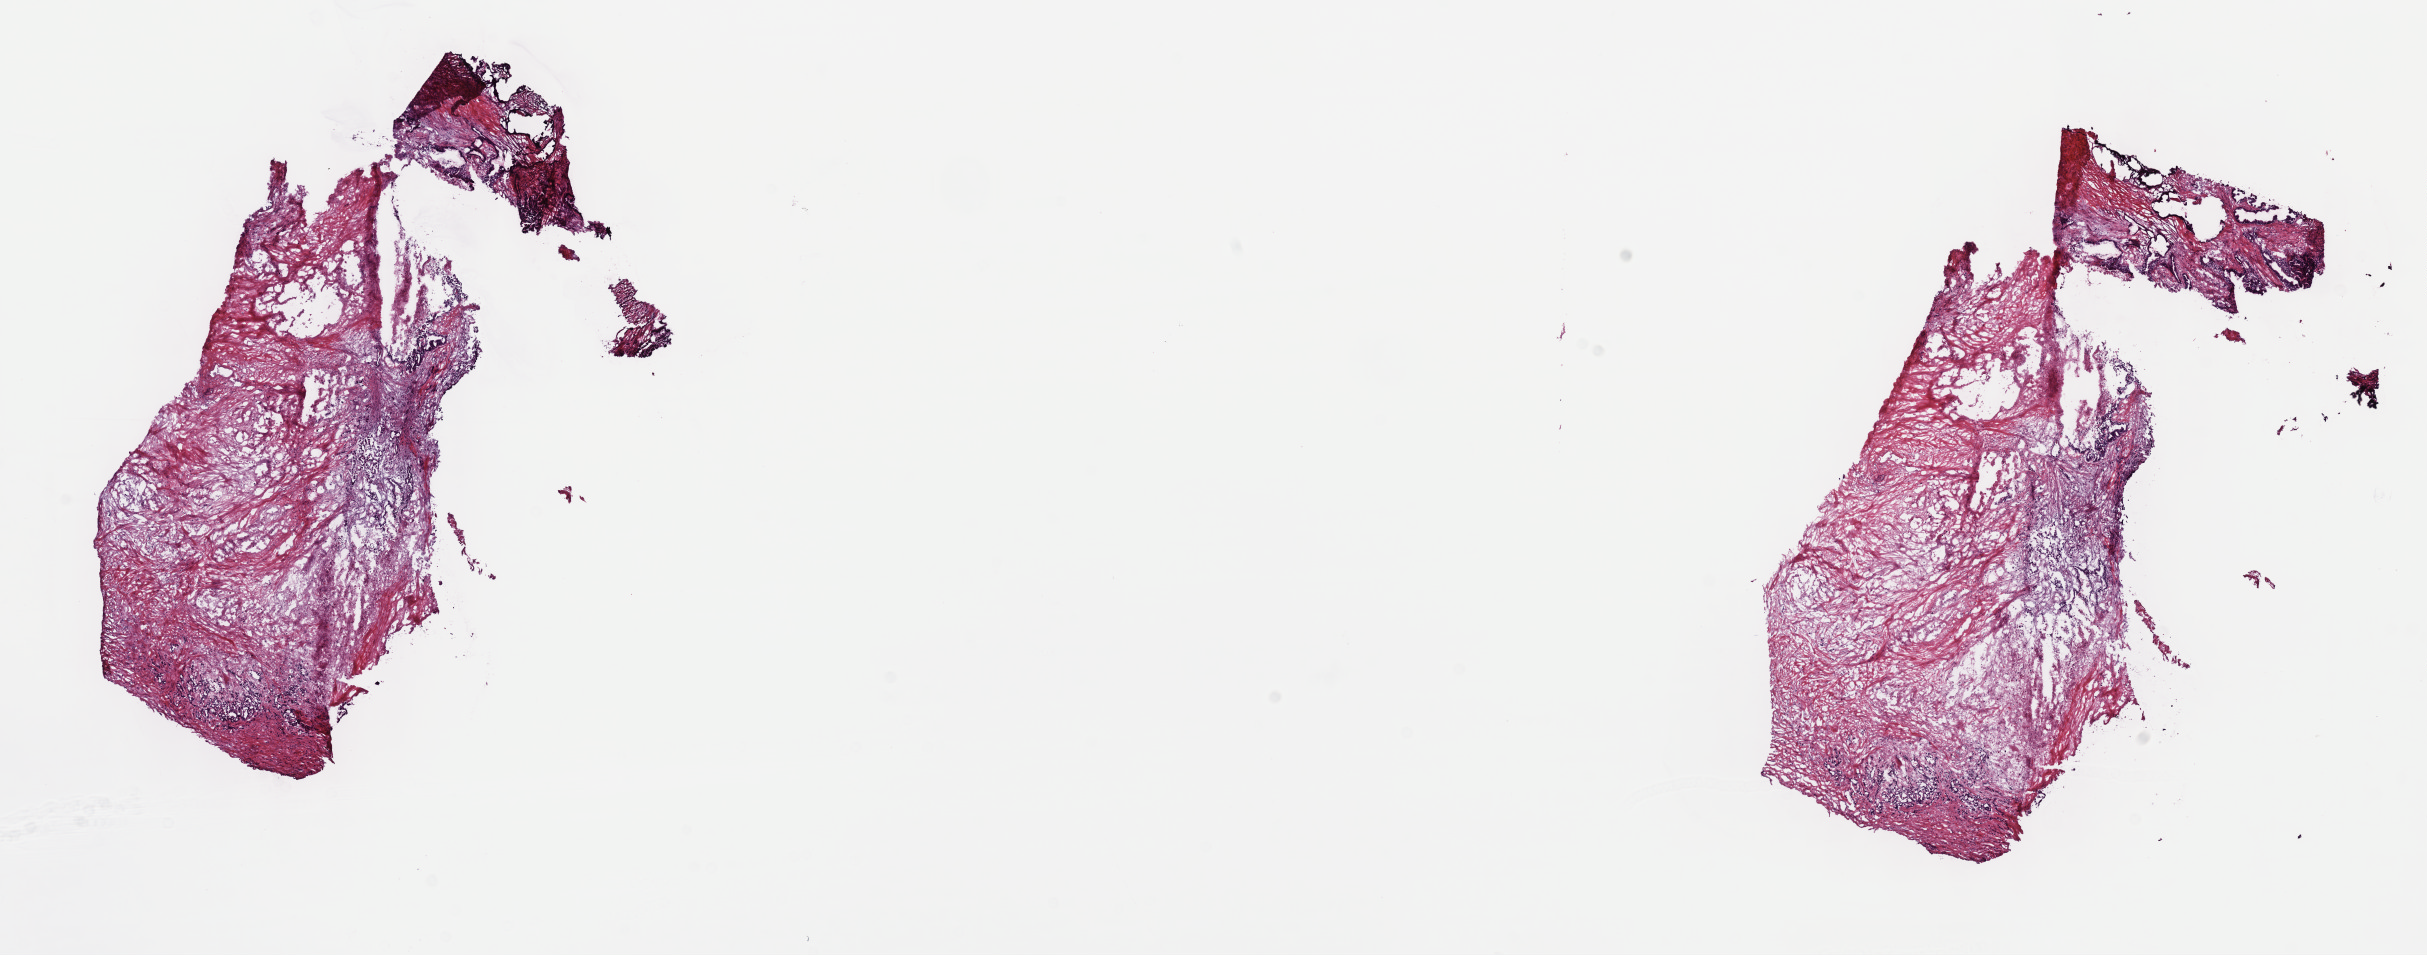
Whole-slide histology image, Hematoxylin and eosin (H&E) stained, shown as a low-resolution overview of the whole scanned area (about 19.6 x 7.7 mm); frozen section; sample: primary tumour, pancreas. Patient: male, age at initial diagnosis 68 years. Histologic grade: G3 (poorly differentiated). Slide review estimates, as recorded: tumour cells 8%, tumour nuclei 85%, normal cells 0%, stromal cells 67%, necrosis 25%. Infiltration values recorded for this section: lymphocyte infiltration 5%, monocyte infiltration 1%, neutrophil infiltration 0%.
TNM: T3 N0 MX. Histologic diagnosis: Infiltrating duct carcinoma, NOS. AJCC pathologic stage: IIA (7th edition).